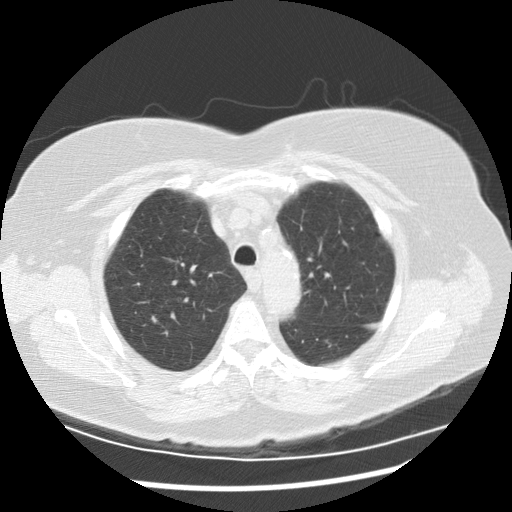
Low-dose screening chest CT, axial slice. Second annual screen. Lung window (W 1500 / L -600 HU). 2.5 mm slice thickness. Standard (soft-tissue) reconstruction kernel (STANDARD). Slice 49 of 225 in the series. 512 × 512 image matrix, field of view 360 × 360 mm. Female, age 72 years at enrolment. Current smoker at enrolment.
Expert-annotated lung lesion, bounding box <134,310,166,335> (left, top, right, bottom; pixels). No non-calcified nodule or mass ≥4 mm was recorded by the screening reader at this exam. Official screen result: negative screen, minor abnormalities not suspicious for lung cancer. Participant outcome: lung cancer diagnosed 507 days after this screen — squamous cell carcinoma, NOS, right upper lobe, poorly differentiated (G3), stage IIIA (AJCC 6th edition), 22 mm at pathology.